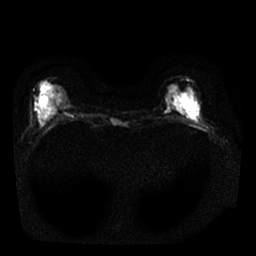
Breast MRI, one axial slice; slice 7 of 25 in the series (ordered by position); diffusion-weighted series; image 2 of 4 stored at this slice position (different b-values; order by instance number); 1.5 T; 256 × 256 image matrix, field of view 320 × 320 mm. Female patient.
Structures marked on this image (expert manual segmentation):
- tumour on diffusion-weighted imaging: box from (x=184, y=102) to (x=188, y=106) px